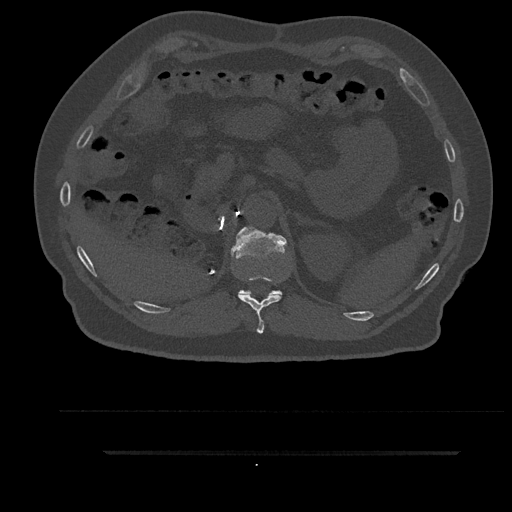
CT including the spine, one axial slice; slice 277 of 797 in the series (ordered by position); reconstruction kernel Br40s/3; 120 kVp; bone window (W 1800 / L 400 HU); 0.5 mm slice thickness; 512 × 512 image matrix. Male patient, age 63 years. Case-level facts recorded for this patient, not image findings: primary cancer: renal; vertebrae with lytic lesions (as recorded): T8.
Annotated regions visible in this slice (semi-automatically segmented with operator editing):
- T11 vertebra: bounding box <238,275,282,334> (left, top, right, bottom; pixels)
- T12 vertebra: <231,226,287,295>